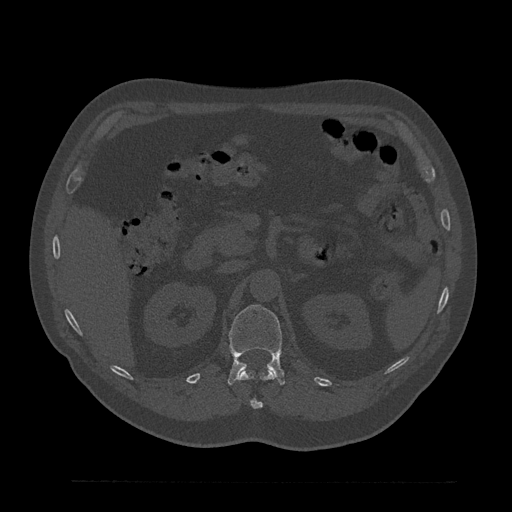
CT including the spine, one axial slice. Position 189 of 797 along the scan axis. 120 kVp. Bone window (W 1800 / L 400 HU). 0.5 mm slice thickness. 512 × 512 image matrix, field of view 430 × 430 mm. Patient: male, 61 years. From the clinical record (not read from this slice): primary cancer: prostate.
Annotated regions visible in this slice (semi-automatically segmented with operator editing):
- L1 vertebra: bounding box (x1, y1, x2, y2) in pixels: (228, 305, 285, 385)
- T12 vertebra: (238, 371, 276, 409)